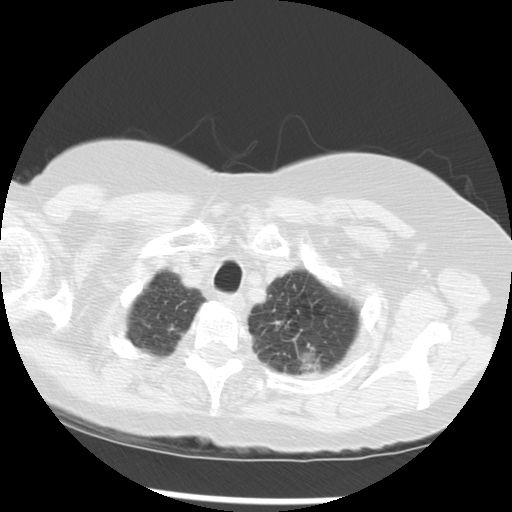
Low-dose screening chest CT, axial slice; third annual screen; lung window (W 1500 / L -600 HU); standard (soft-tissue) reconstruction kernel (STANDARD); 120 kVp; slice 251 of 283 in the series; 512 × 512 image matrix. Female participant, aged 70 years at enrolment. Current smoker at enrolment.
Expert-annotated lung lesion, bounding box <241,298,342,386> (left, top, right, bottom; pixels). Screening reader's record for this exam (one nodule recorded; not confirmed to be the boxed lesion): non-calcified nodule or mass ≥4 mm, left upper lobe, 32 × 26 mm, spiculated (stellate) margins, soft tissue attenuation, pre-existing on the prior screen: yes; interval growth: yes. Official screen result: positive, other. Lung cancer was diagnosed 24 days after this screen: neoplasm, malignant, left upper lobe, stage IIIB (AJCC 6th edition), 40 mm at pathology.